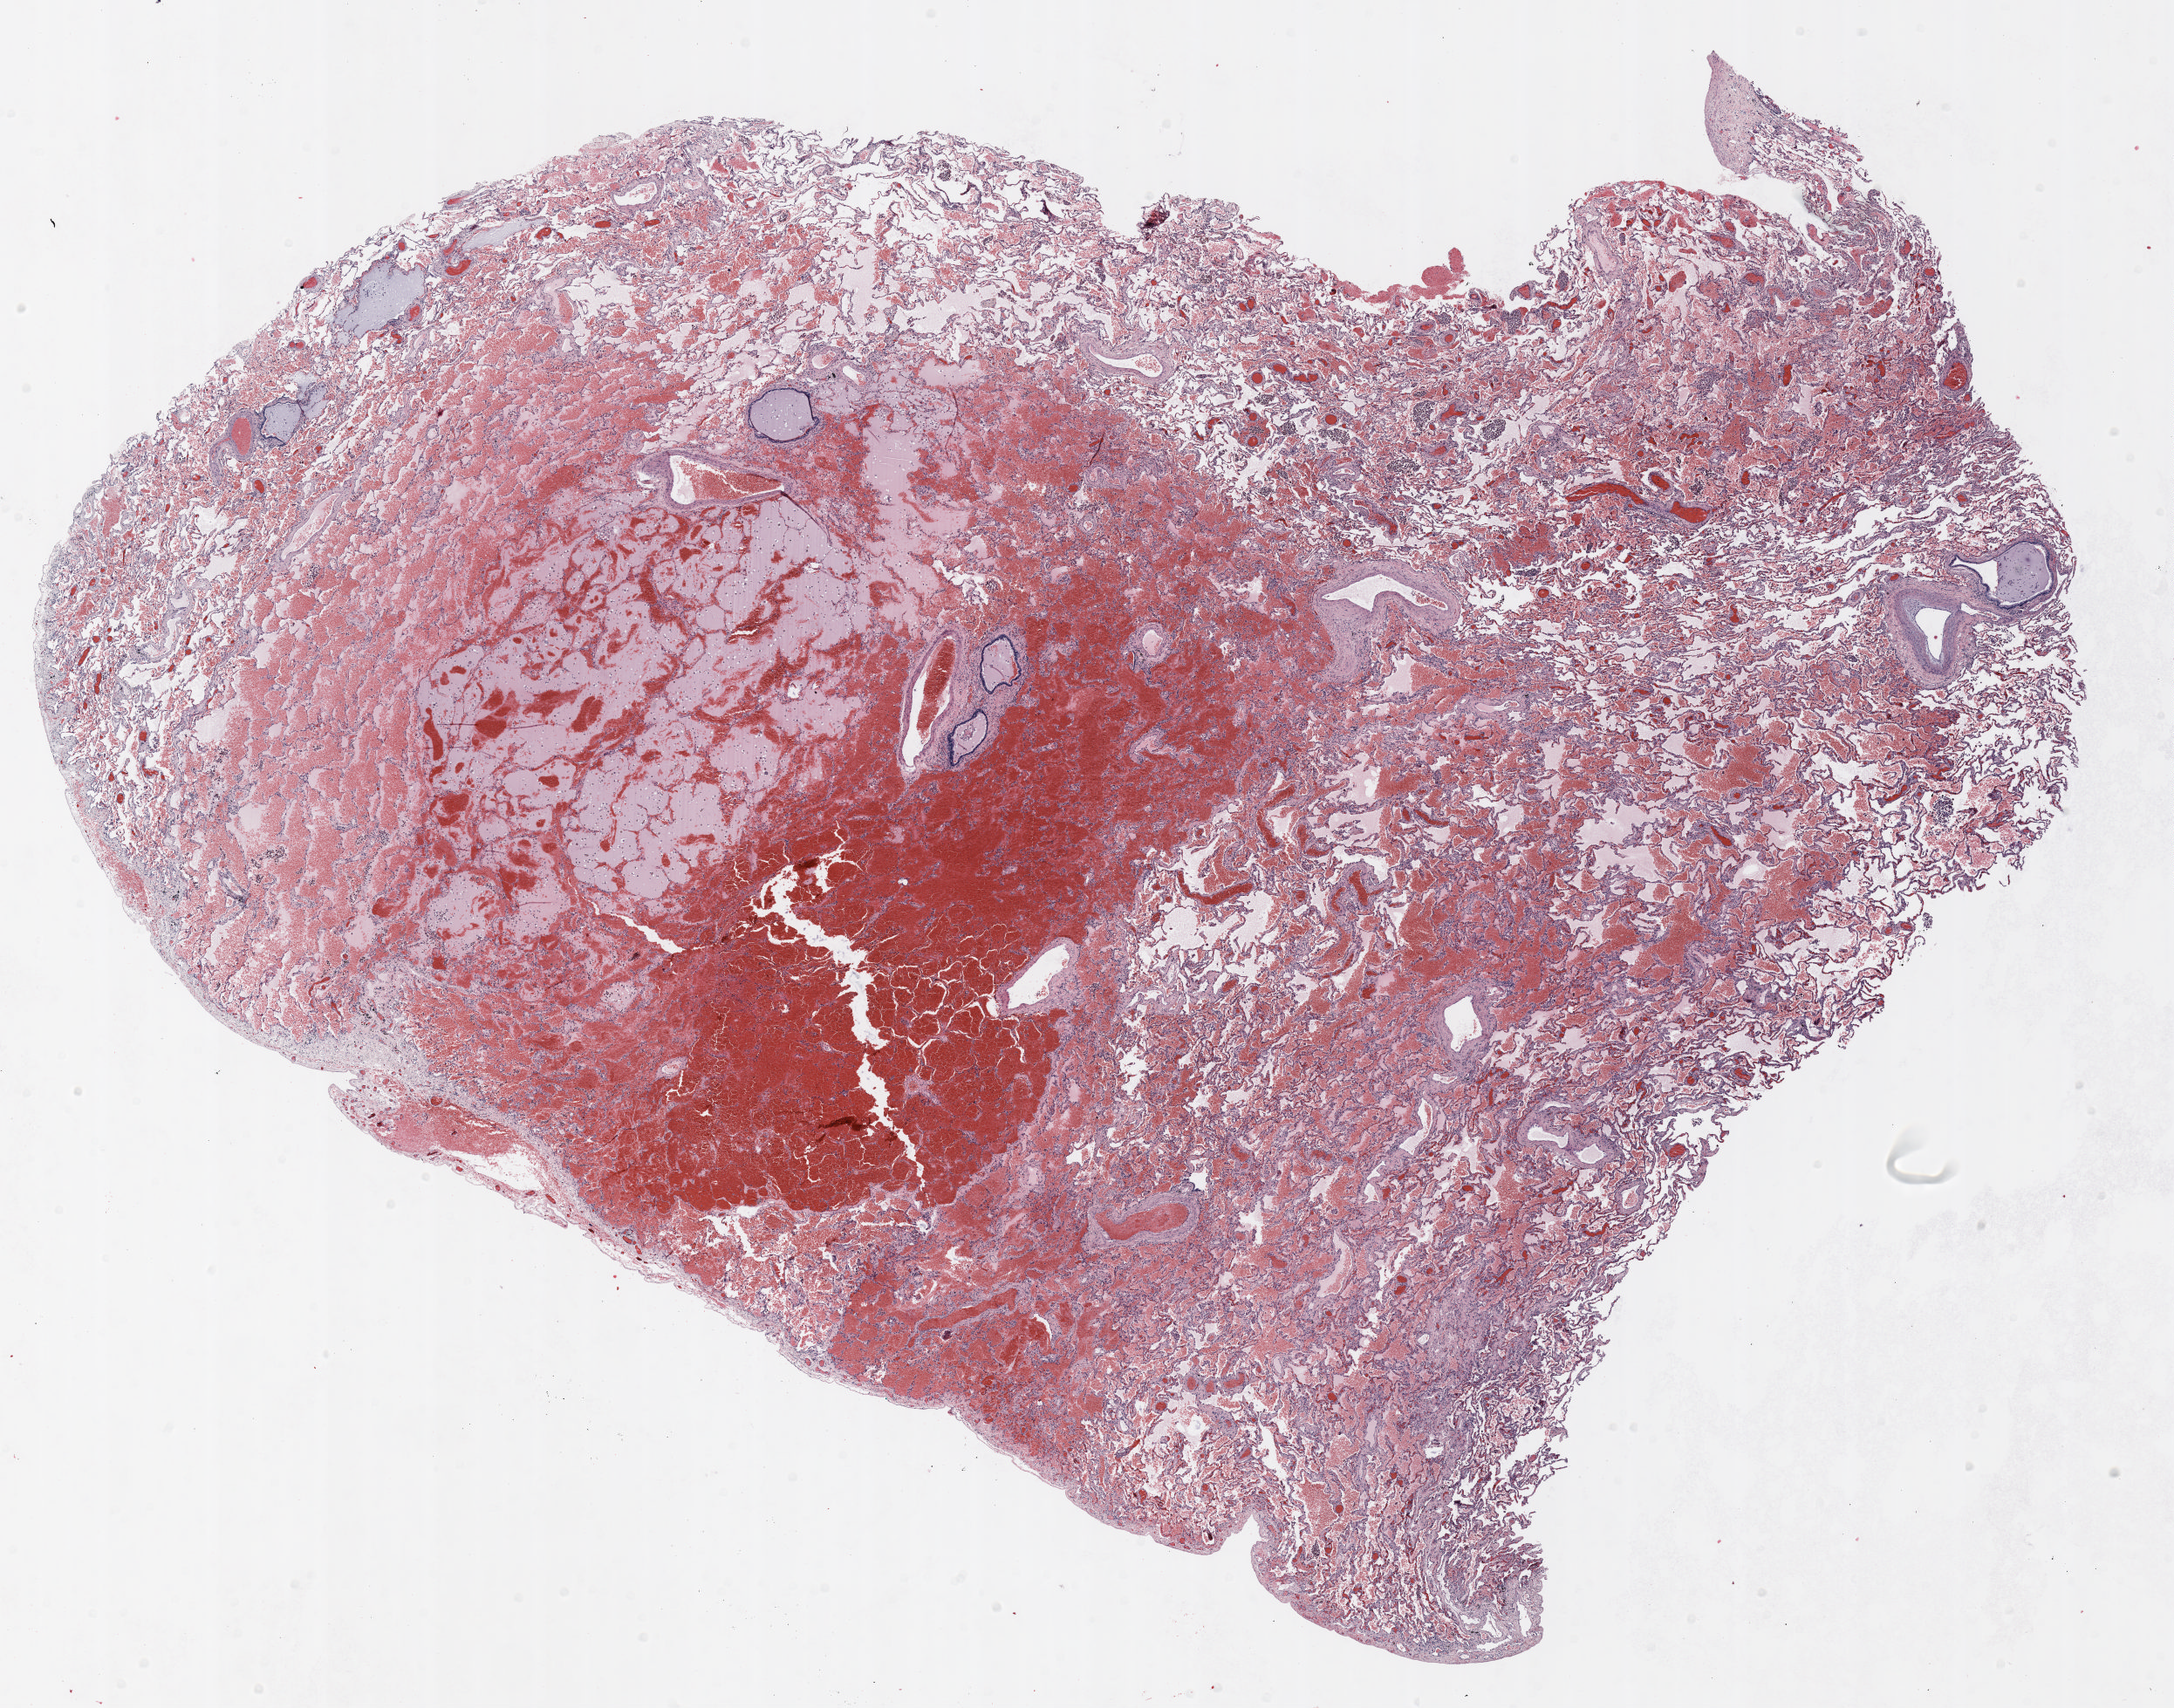
Hematoxylin and eosin (H&E) stained whole-slide image — shown as a low-resolution overview of the whole scanned area (about 20.0 x 15.7 mm, slide scanned at 20x). FFPE section. Lung. Female, age 58 at enrolment. Current smoker at enrolment. Grade: moderately differentiated (G2).
- primary tumour location (clinical record): right upper lobe
- participant's lung-cancer diagnosis: Squamous cell carcinoma, NOS (ICD-O-3 8070/3)
- tumour size (pathology): 17 mm
- stage (AJCC 6th edition): IA